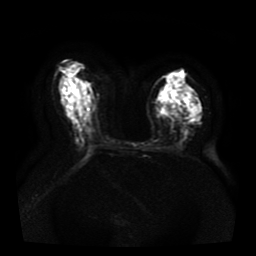
Breast MRI, one axial slice; slice 23 of 41 in the series (ordered by position); diffusion-weighted series; image 2 of 4 stored at this slice position (different b-values; order by instance number); 1.5 T; 256 × 256 image matrix. Female patient.
Structures marked on this image (outlined manually by an expert reader):
- tumour on diffusion-weighted imaging: box from (x=178, y=107) to (x=182, y=113) px